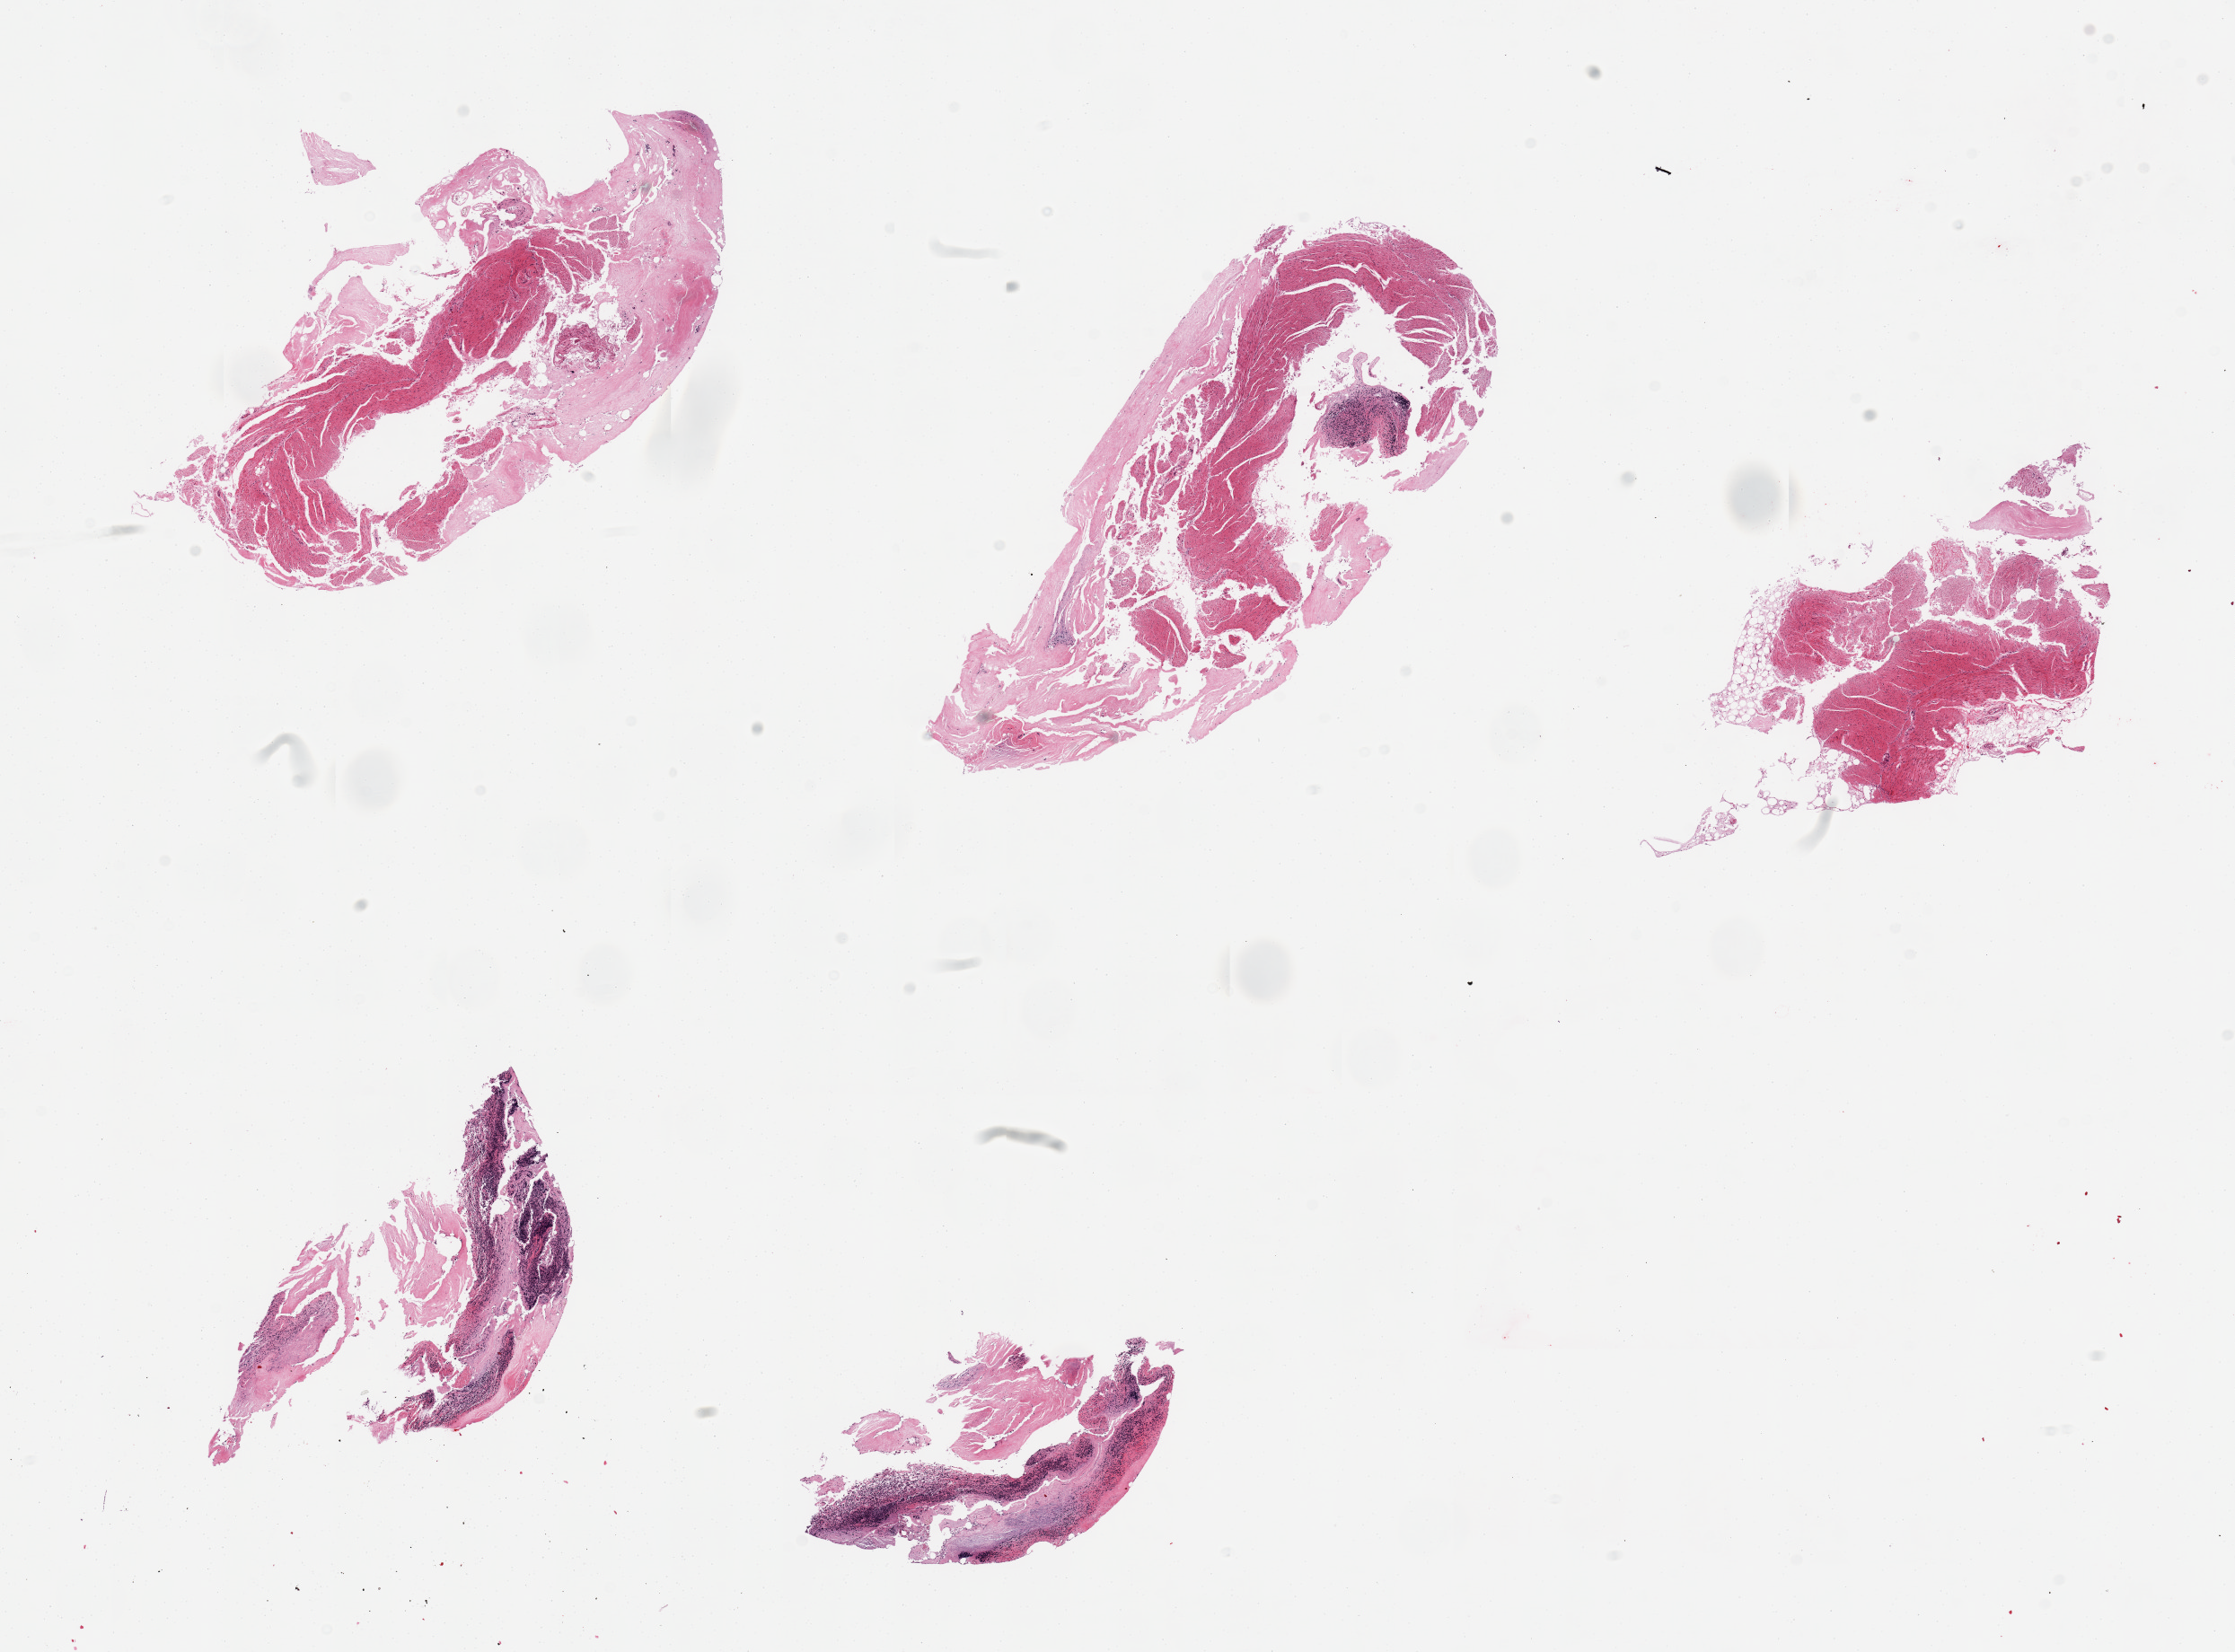
Digitized H&E-stained section, brightfield — low-resolution overview of the scanned area, about 19.7 x 14.6 mm (slide scanned at 20x). Donor sex: male.
Specimen: PAXgene-fixed, paraffin-embedded tissue; section of ileum (target tissue); donor tissue sample.